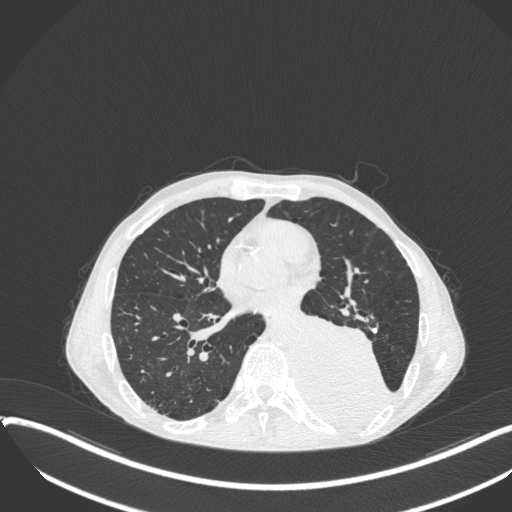
Chest CT, one axial slice. Position 159 of 400 along the scan axis. Reconstruction kernel B31f. Lung window (W 1500 / L -600 HU). 512 × 512 image matrix, field of view 400 × 400 mm. Male patient, age 57 years. Case-level facts recorded for this patient, not image findings: clinical TNM (as recorded): T4 N0 M0.
Outlined on this slice (rectangle marked by the reading radiologist):
- lung tumour (recorded histology: squamous cell carcinoma): box from (x=297, y=311) to (x=394, y=430) px